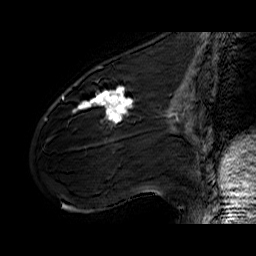
Breast MRI (dynamic contrast-enhanced), one sagittal slice; slice 22 of 60 in the series (ordered by position); dynamic contrast-enhanced series, time point 2 of 6 at this slice position (early post-contrast); 1.5 T; TE 6.4 ms, TR 32.9 ms; 256 × 256 image matrix, field of view 200 × 200 mm. Female patient. From the clinical record (not read from this slice): setting: breast cancer imaged before/during neoadjuvant chemotherapy; receptor status: HER2-positive.
Structures marked on this image (semi-automatic segmentation, software-assisted and operator-edited):
- analysis volume of interest (the breast-tissue region the enhancement analysis was run in; not a lesion): box from (x=61, y=77) to (x=141, y=142) px
- tumour enhancement mask (voxels above the 100 % enhancement threshold inside the analysis volume of interest): (x=62, y=86)–(x=134, y=127)